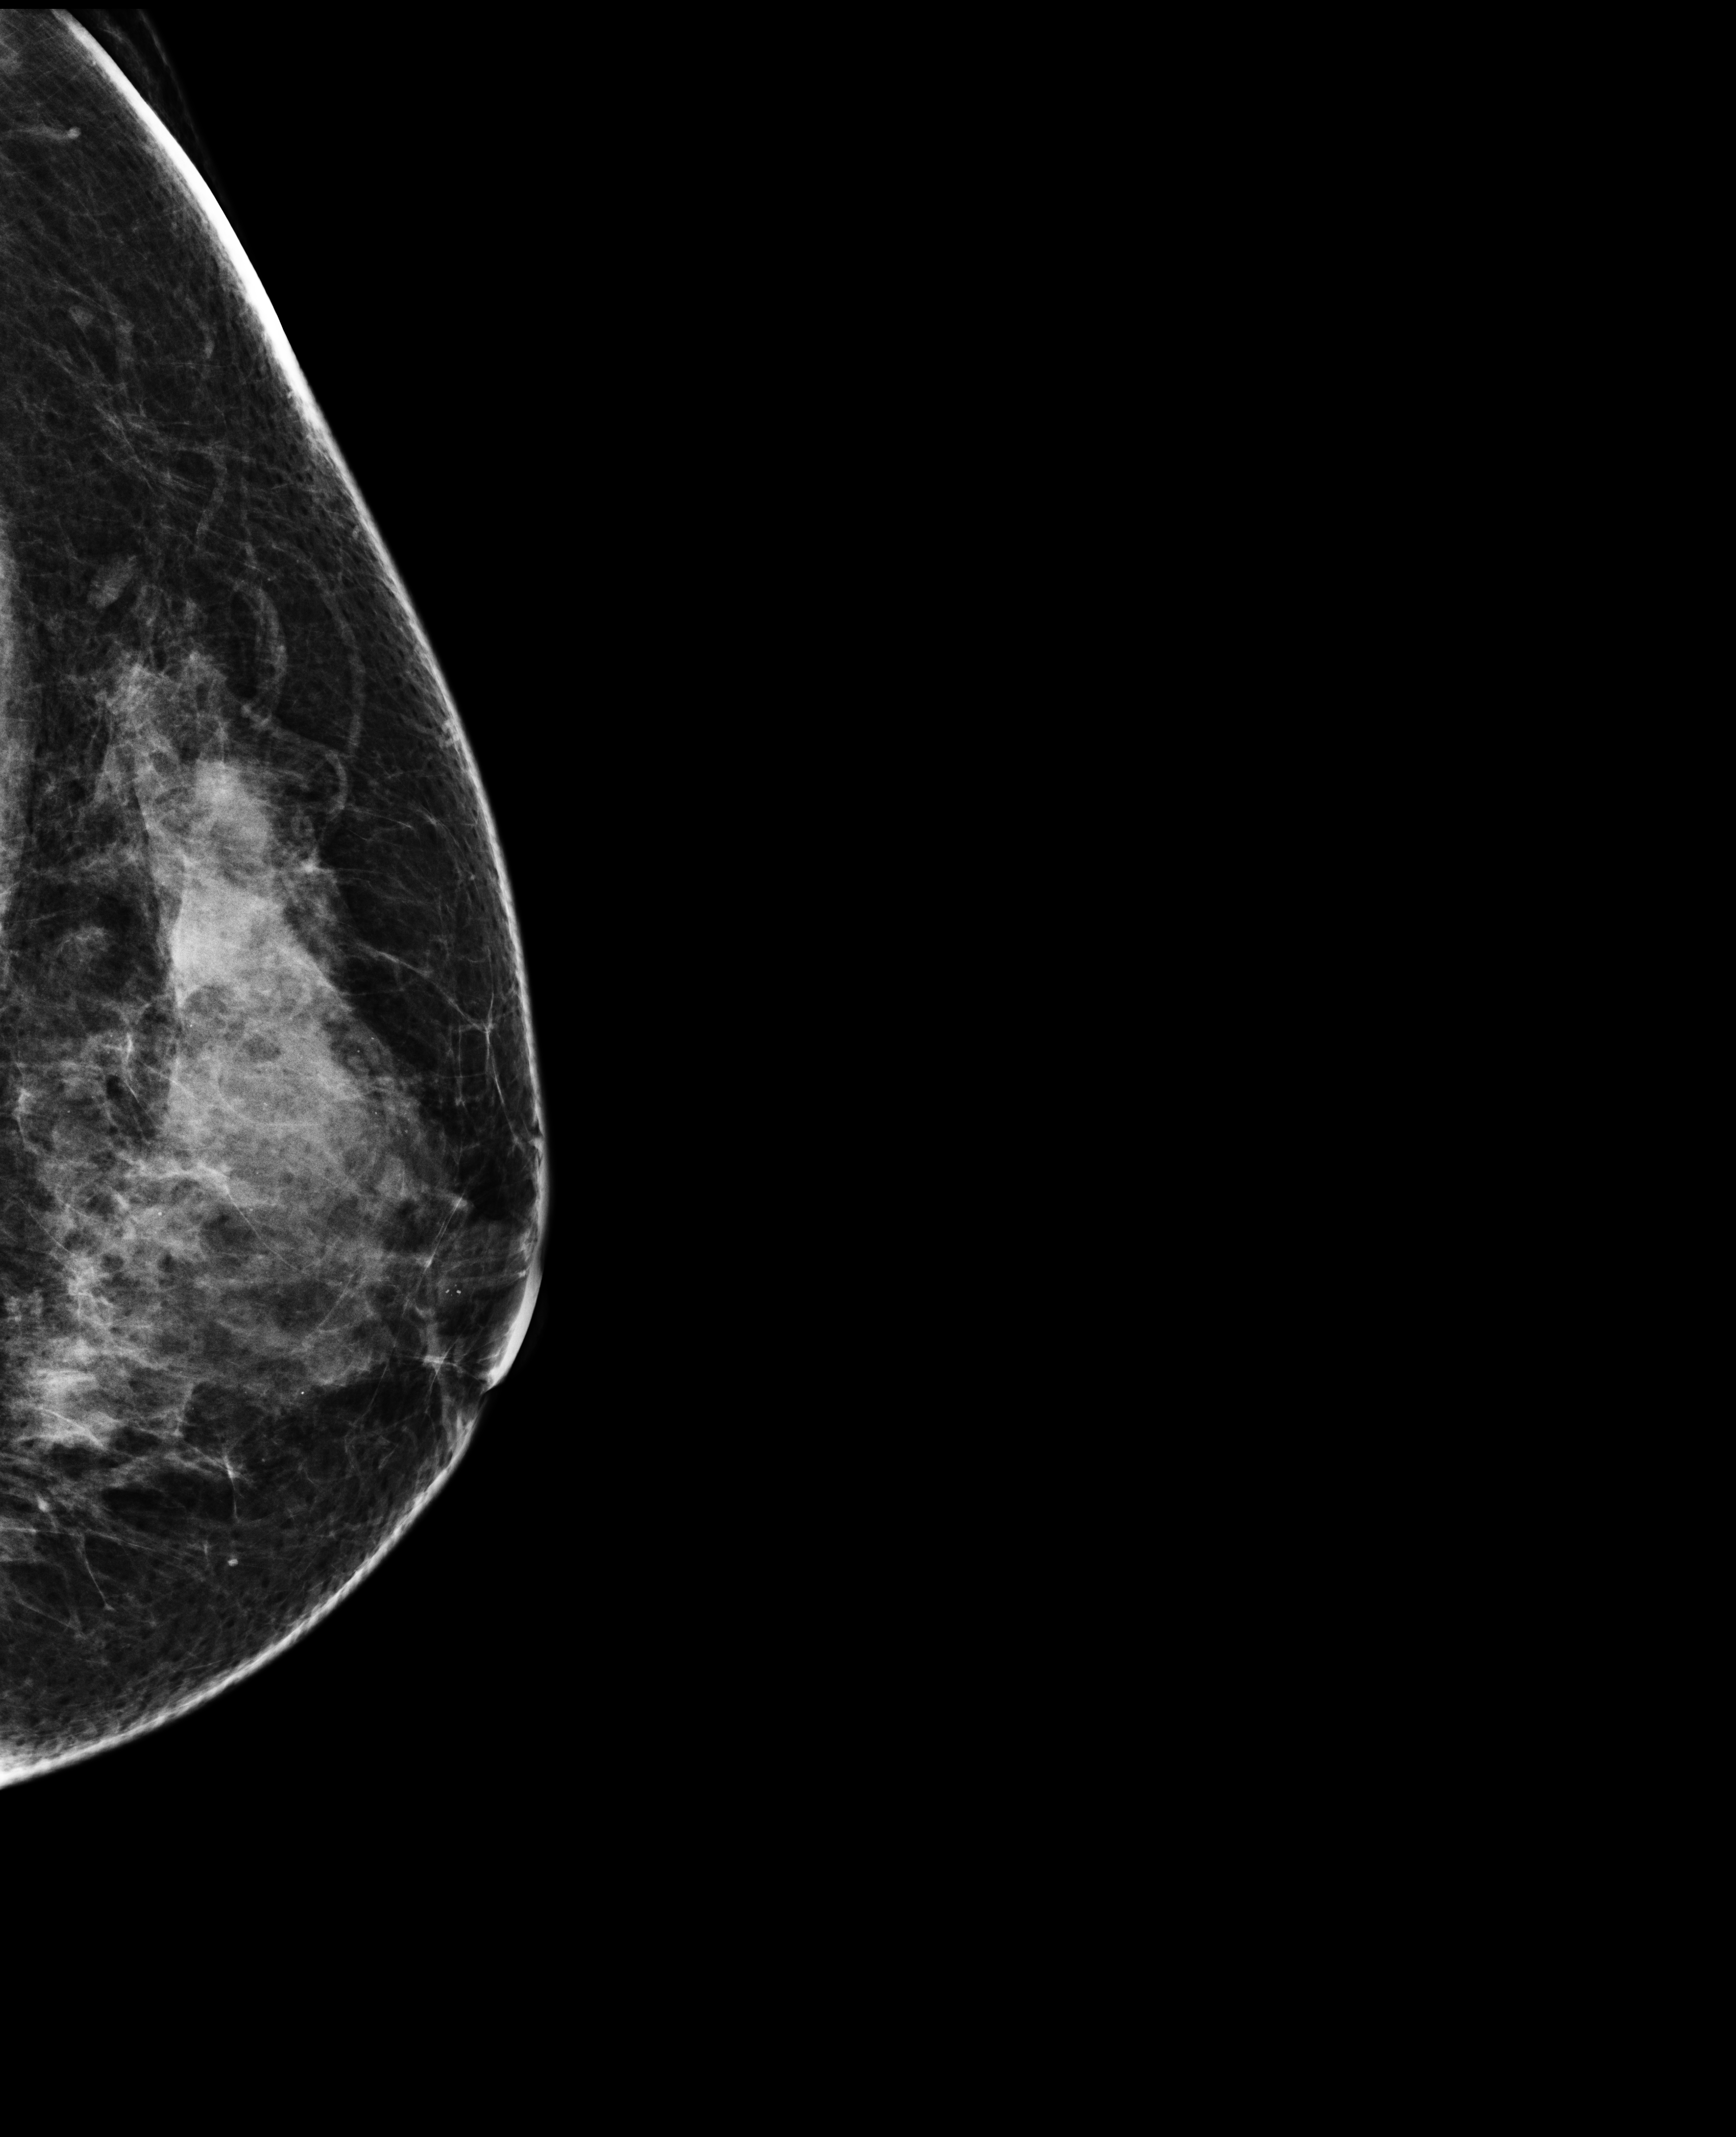
Annual screening mammography examination, compressed breast thickness 64 mm. Female patient, age 49 years.
Image type: full-field digital mammogram. Breast: left. Projection: laterally exaggerated craniocaudal (XCCL) view.